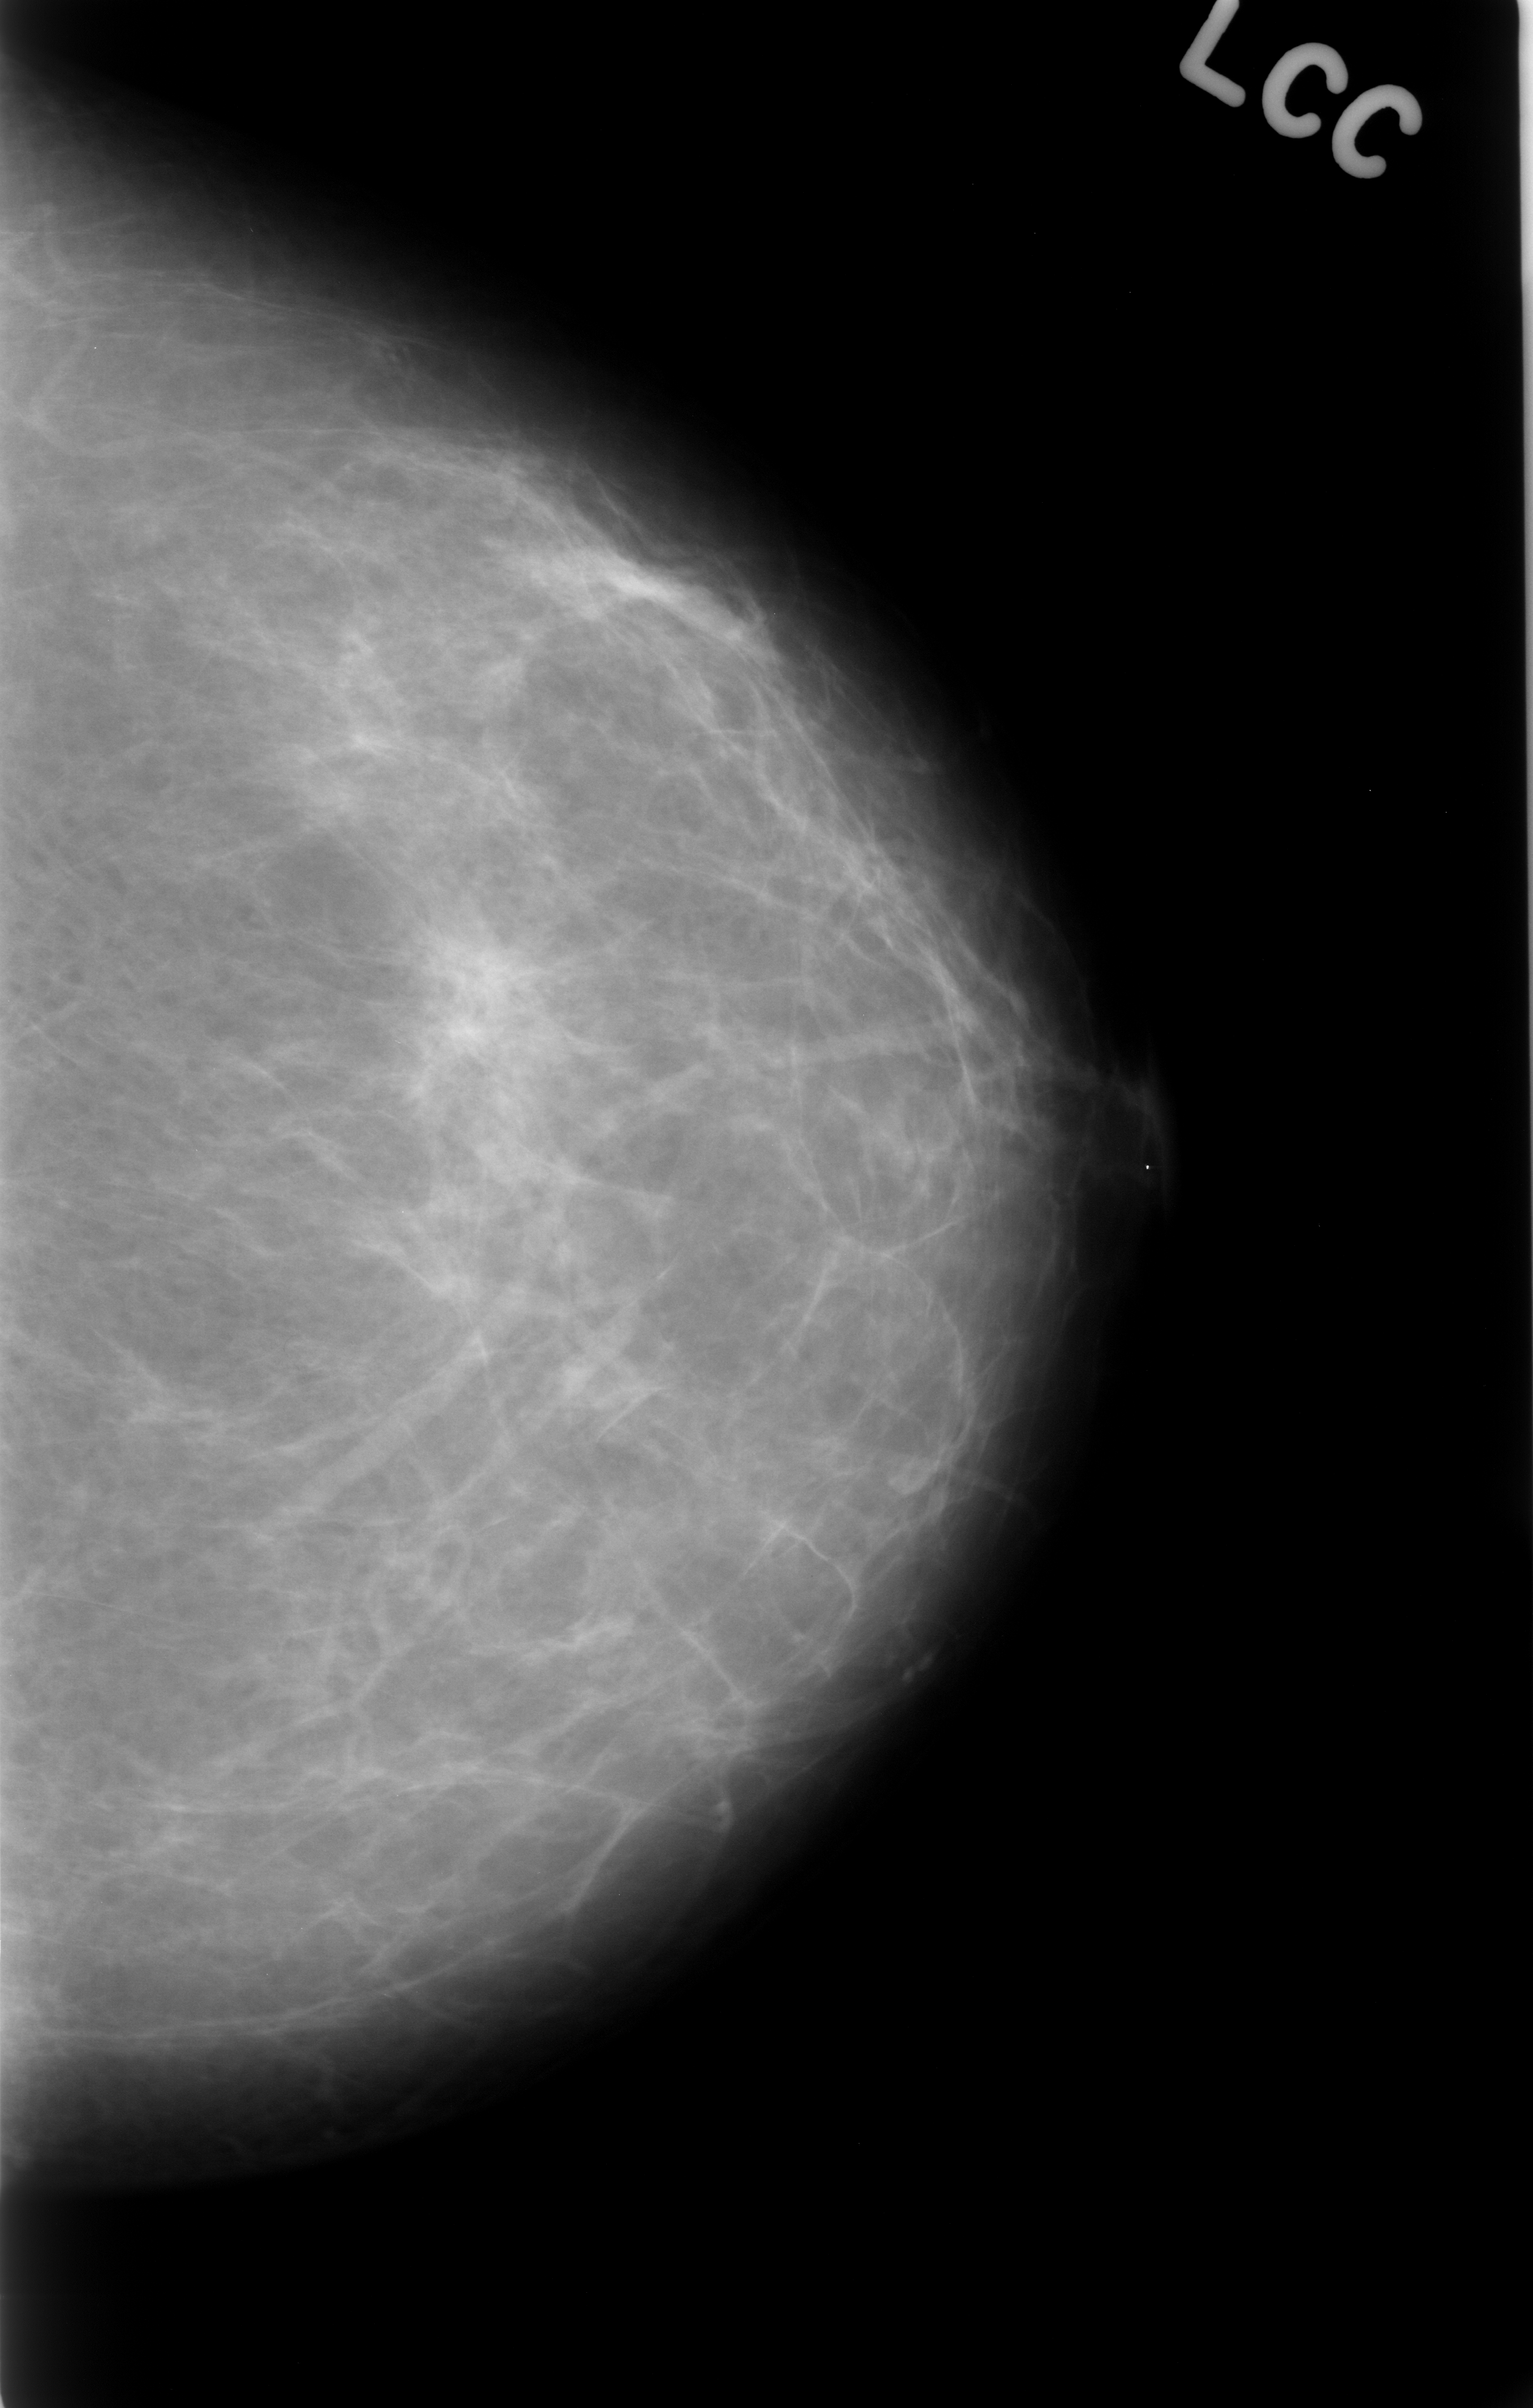
Mammogram (digitized film). Left breast. Craniocaudal (CC) view. 1533 × 2408 image matrix.
Expert-marked regions of interest on this image (one box per marked abnormality):
- mass, shape architectural distortion; BI-RADS assessment category 3; subtlety rating 5 on a 1 (subtle) to 5 (obvious) scale; outcome (as recorded, no biopsy): benign without callback (not worked up further): bounding box [x1, y1, x2, y2] px = [350, 904, 582, 1137]